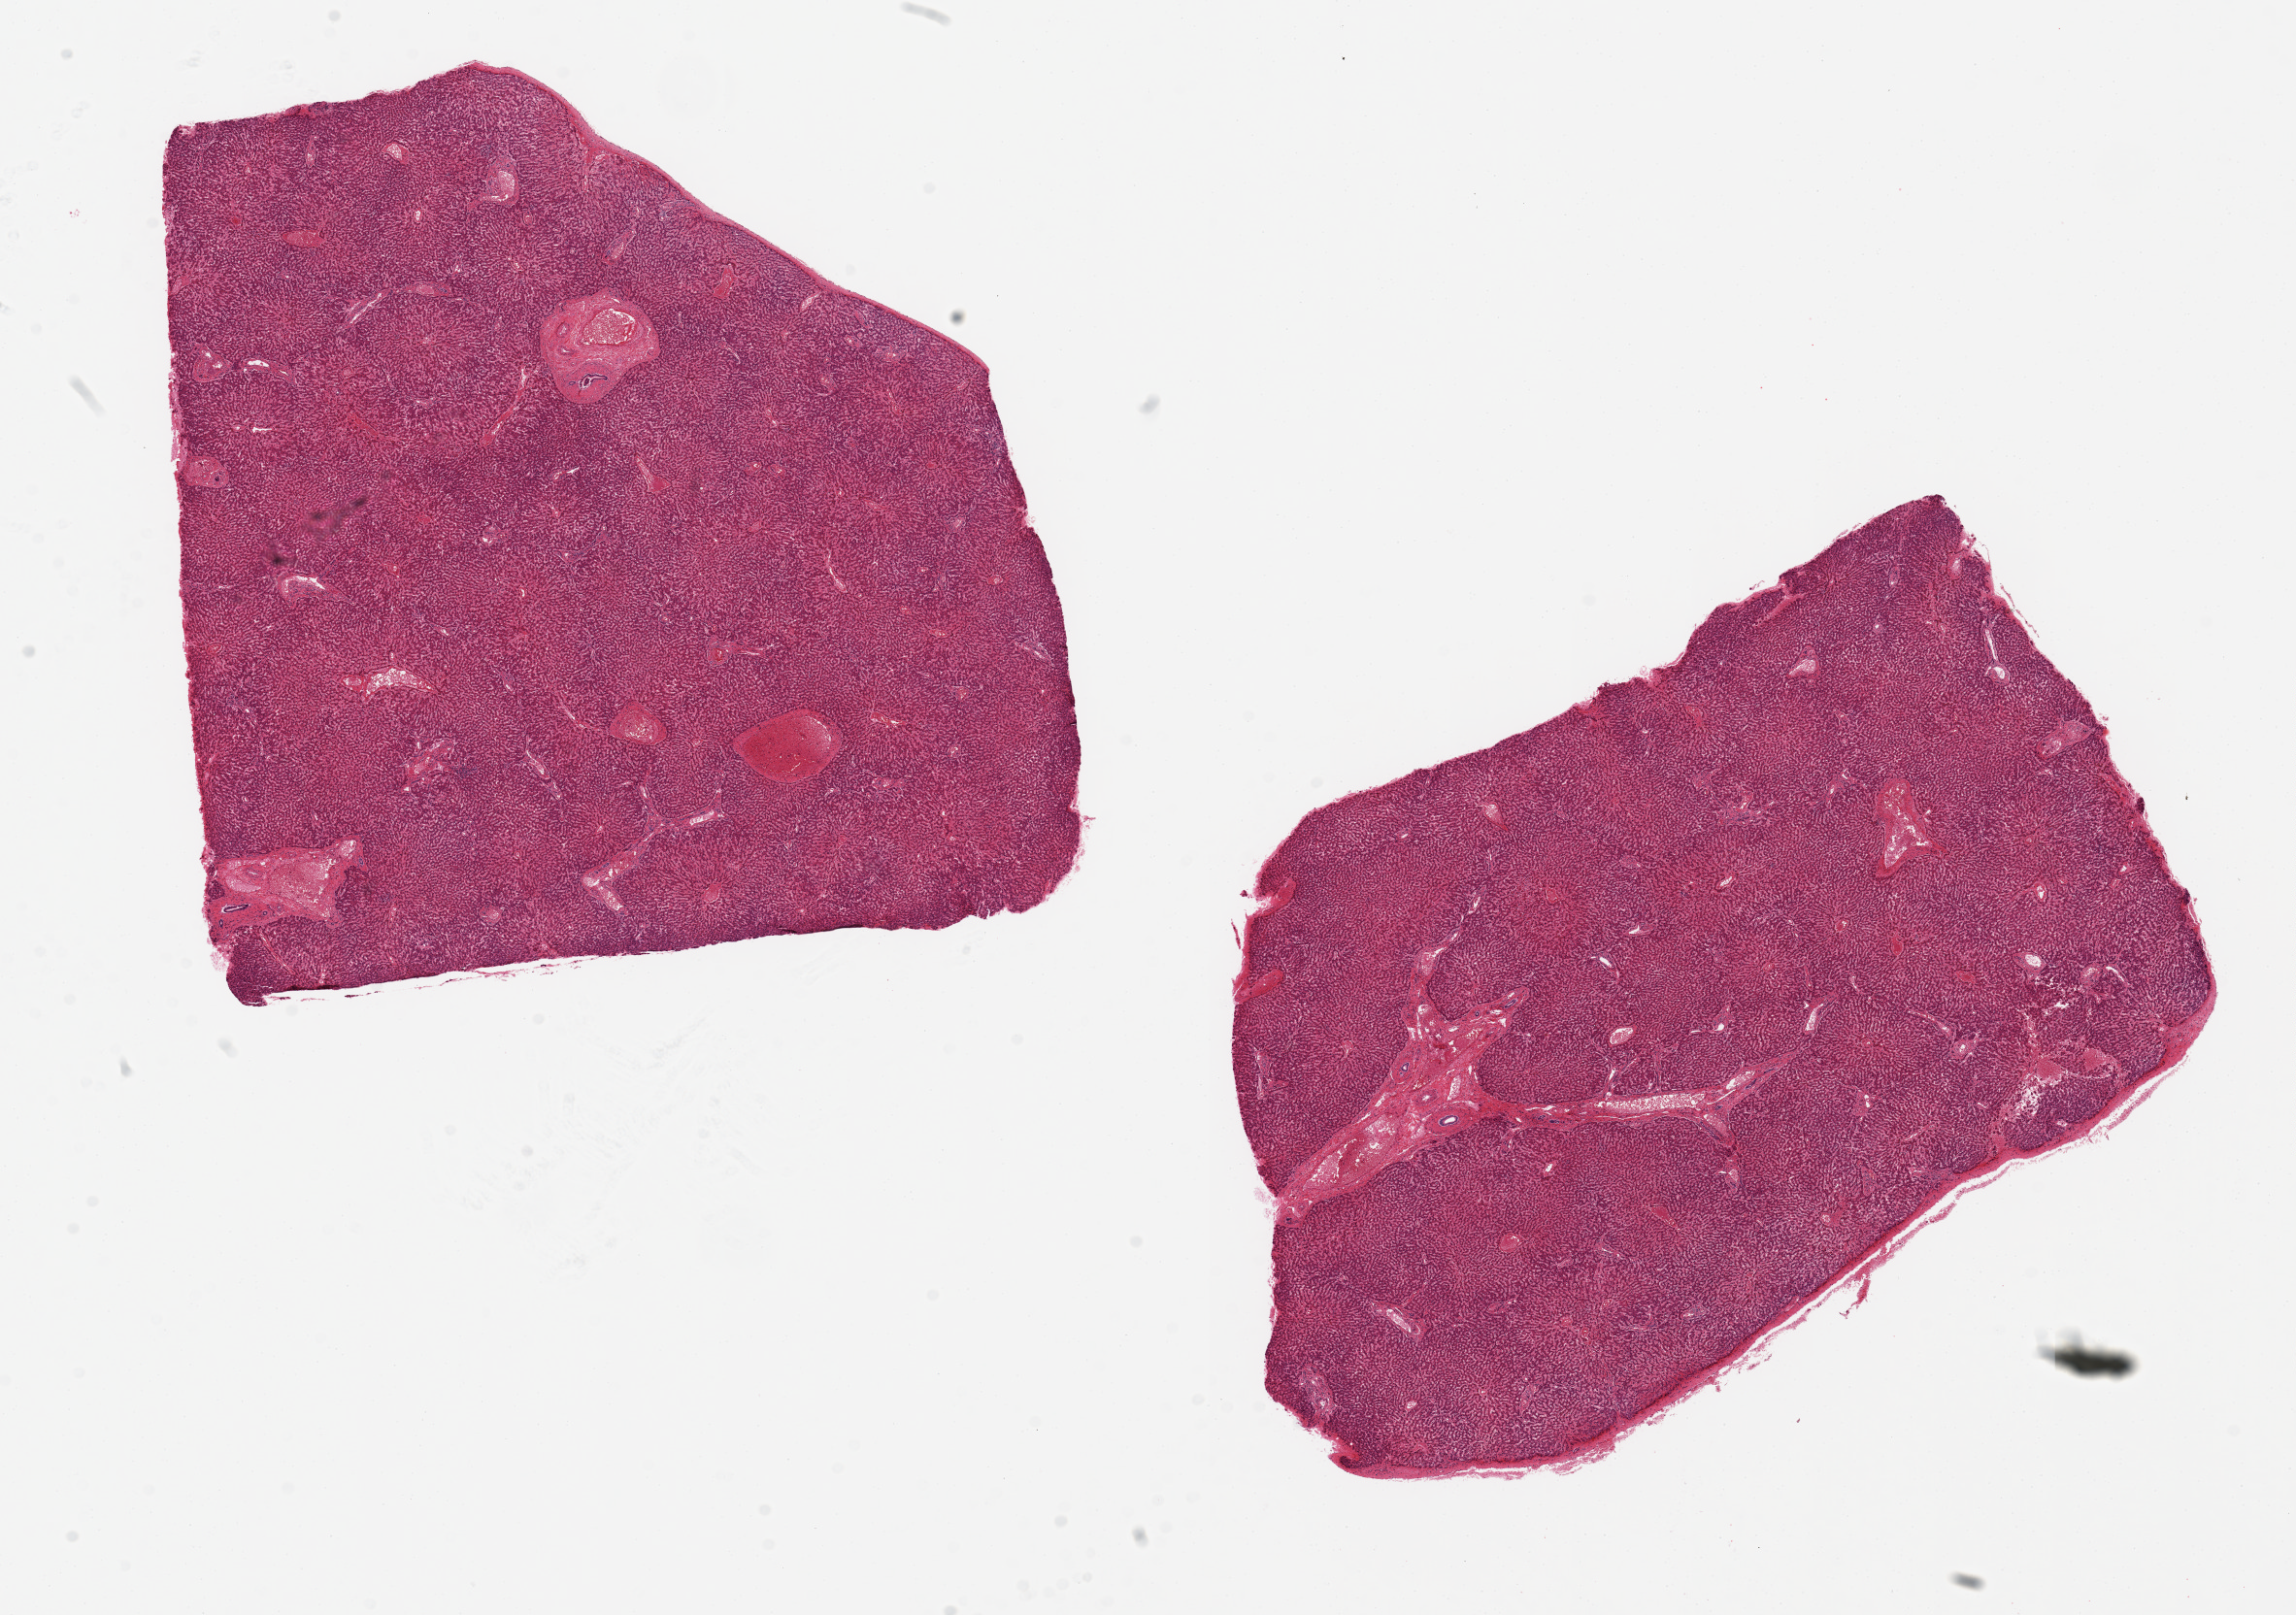
Hematoxylin and eosin (H&E) whole-slide image, brightfield — shown as a low-resolution overview of the whole scanned area (about 18.7 x 13.2 mm, from a 20x scan). PAXgene-fixed paraffin-embedded (PFPE) section. Section of liver (target tissue). Donor tissue sample.
Review note (as recorded): 2 pieces 8x5 & 7x7 mm; not congested.